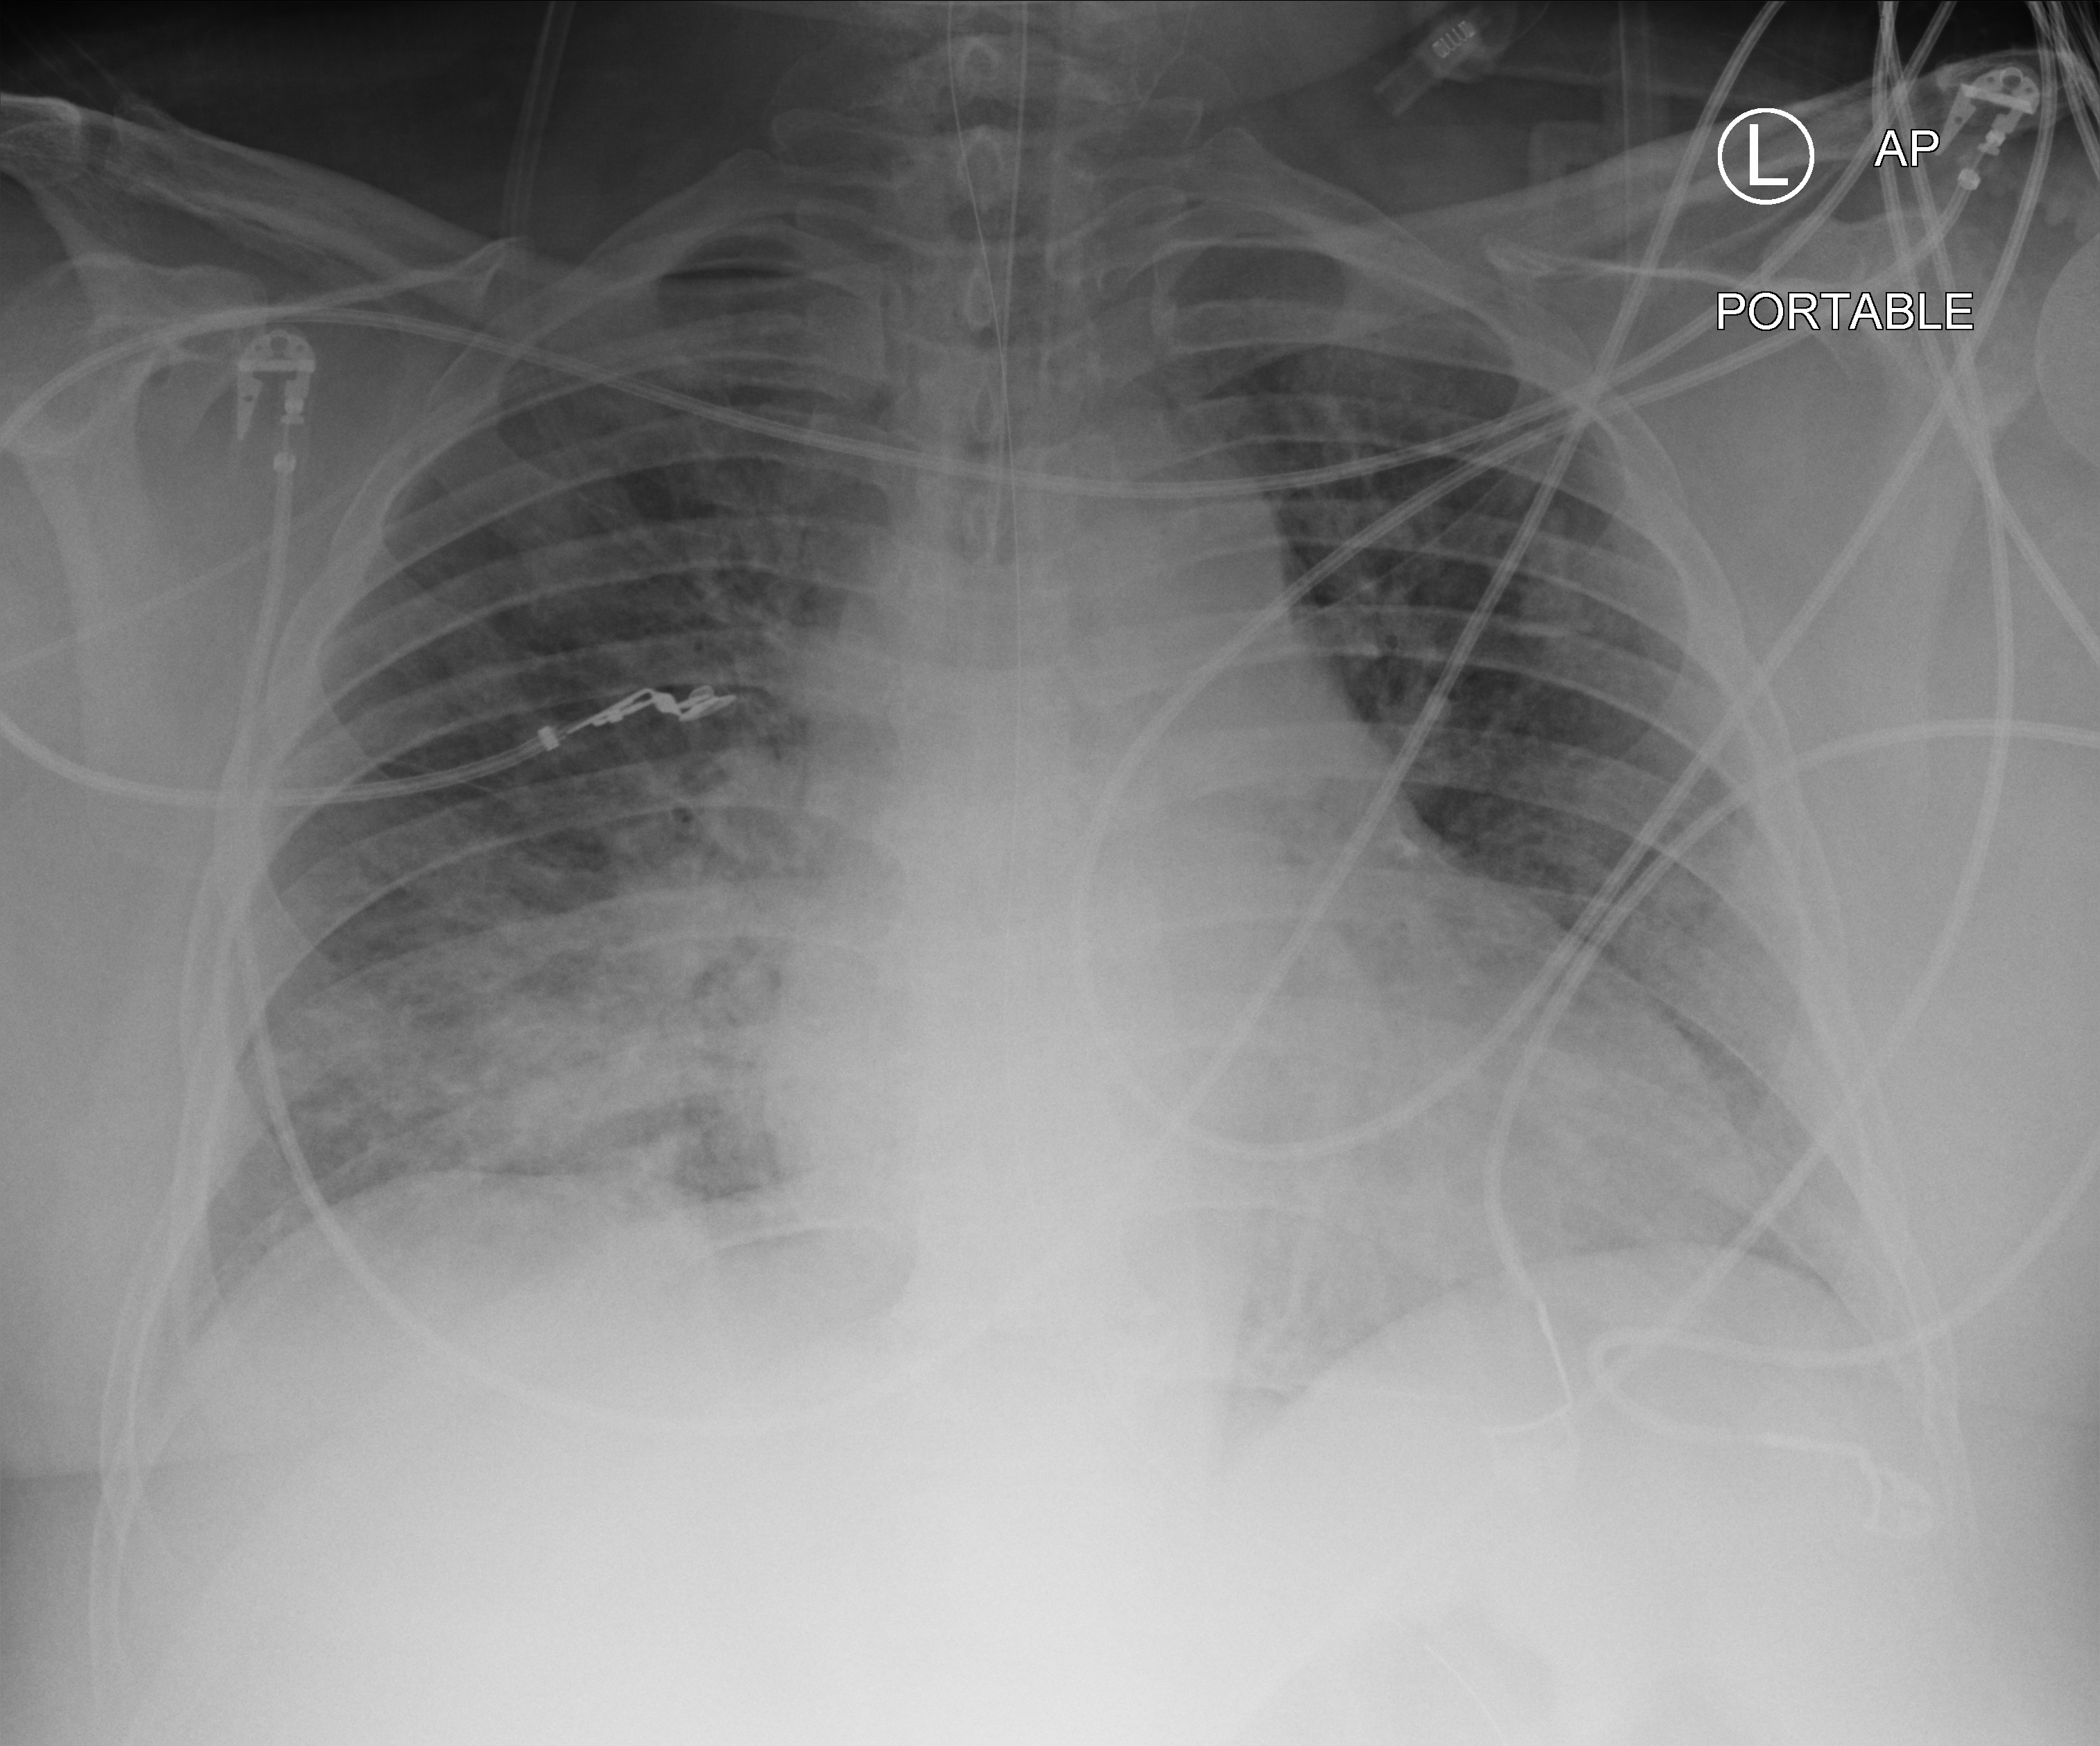
Chest X-ray (portable), anteroposterior (AP) projection. Male patient hospitalised with COVID-19, age 18–59 years.
Hospital-stay facts (about this admission, not read from this image; timing relative to this image not recorded): mechanically ventilated during this hospital stay: yes; admitted to intensive care during this hospital stay: yes; diabetes (admission record): yes.